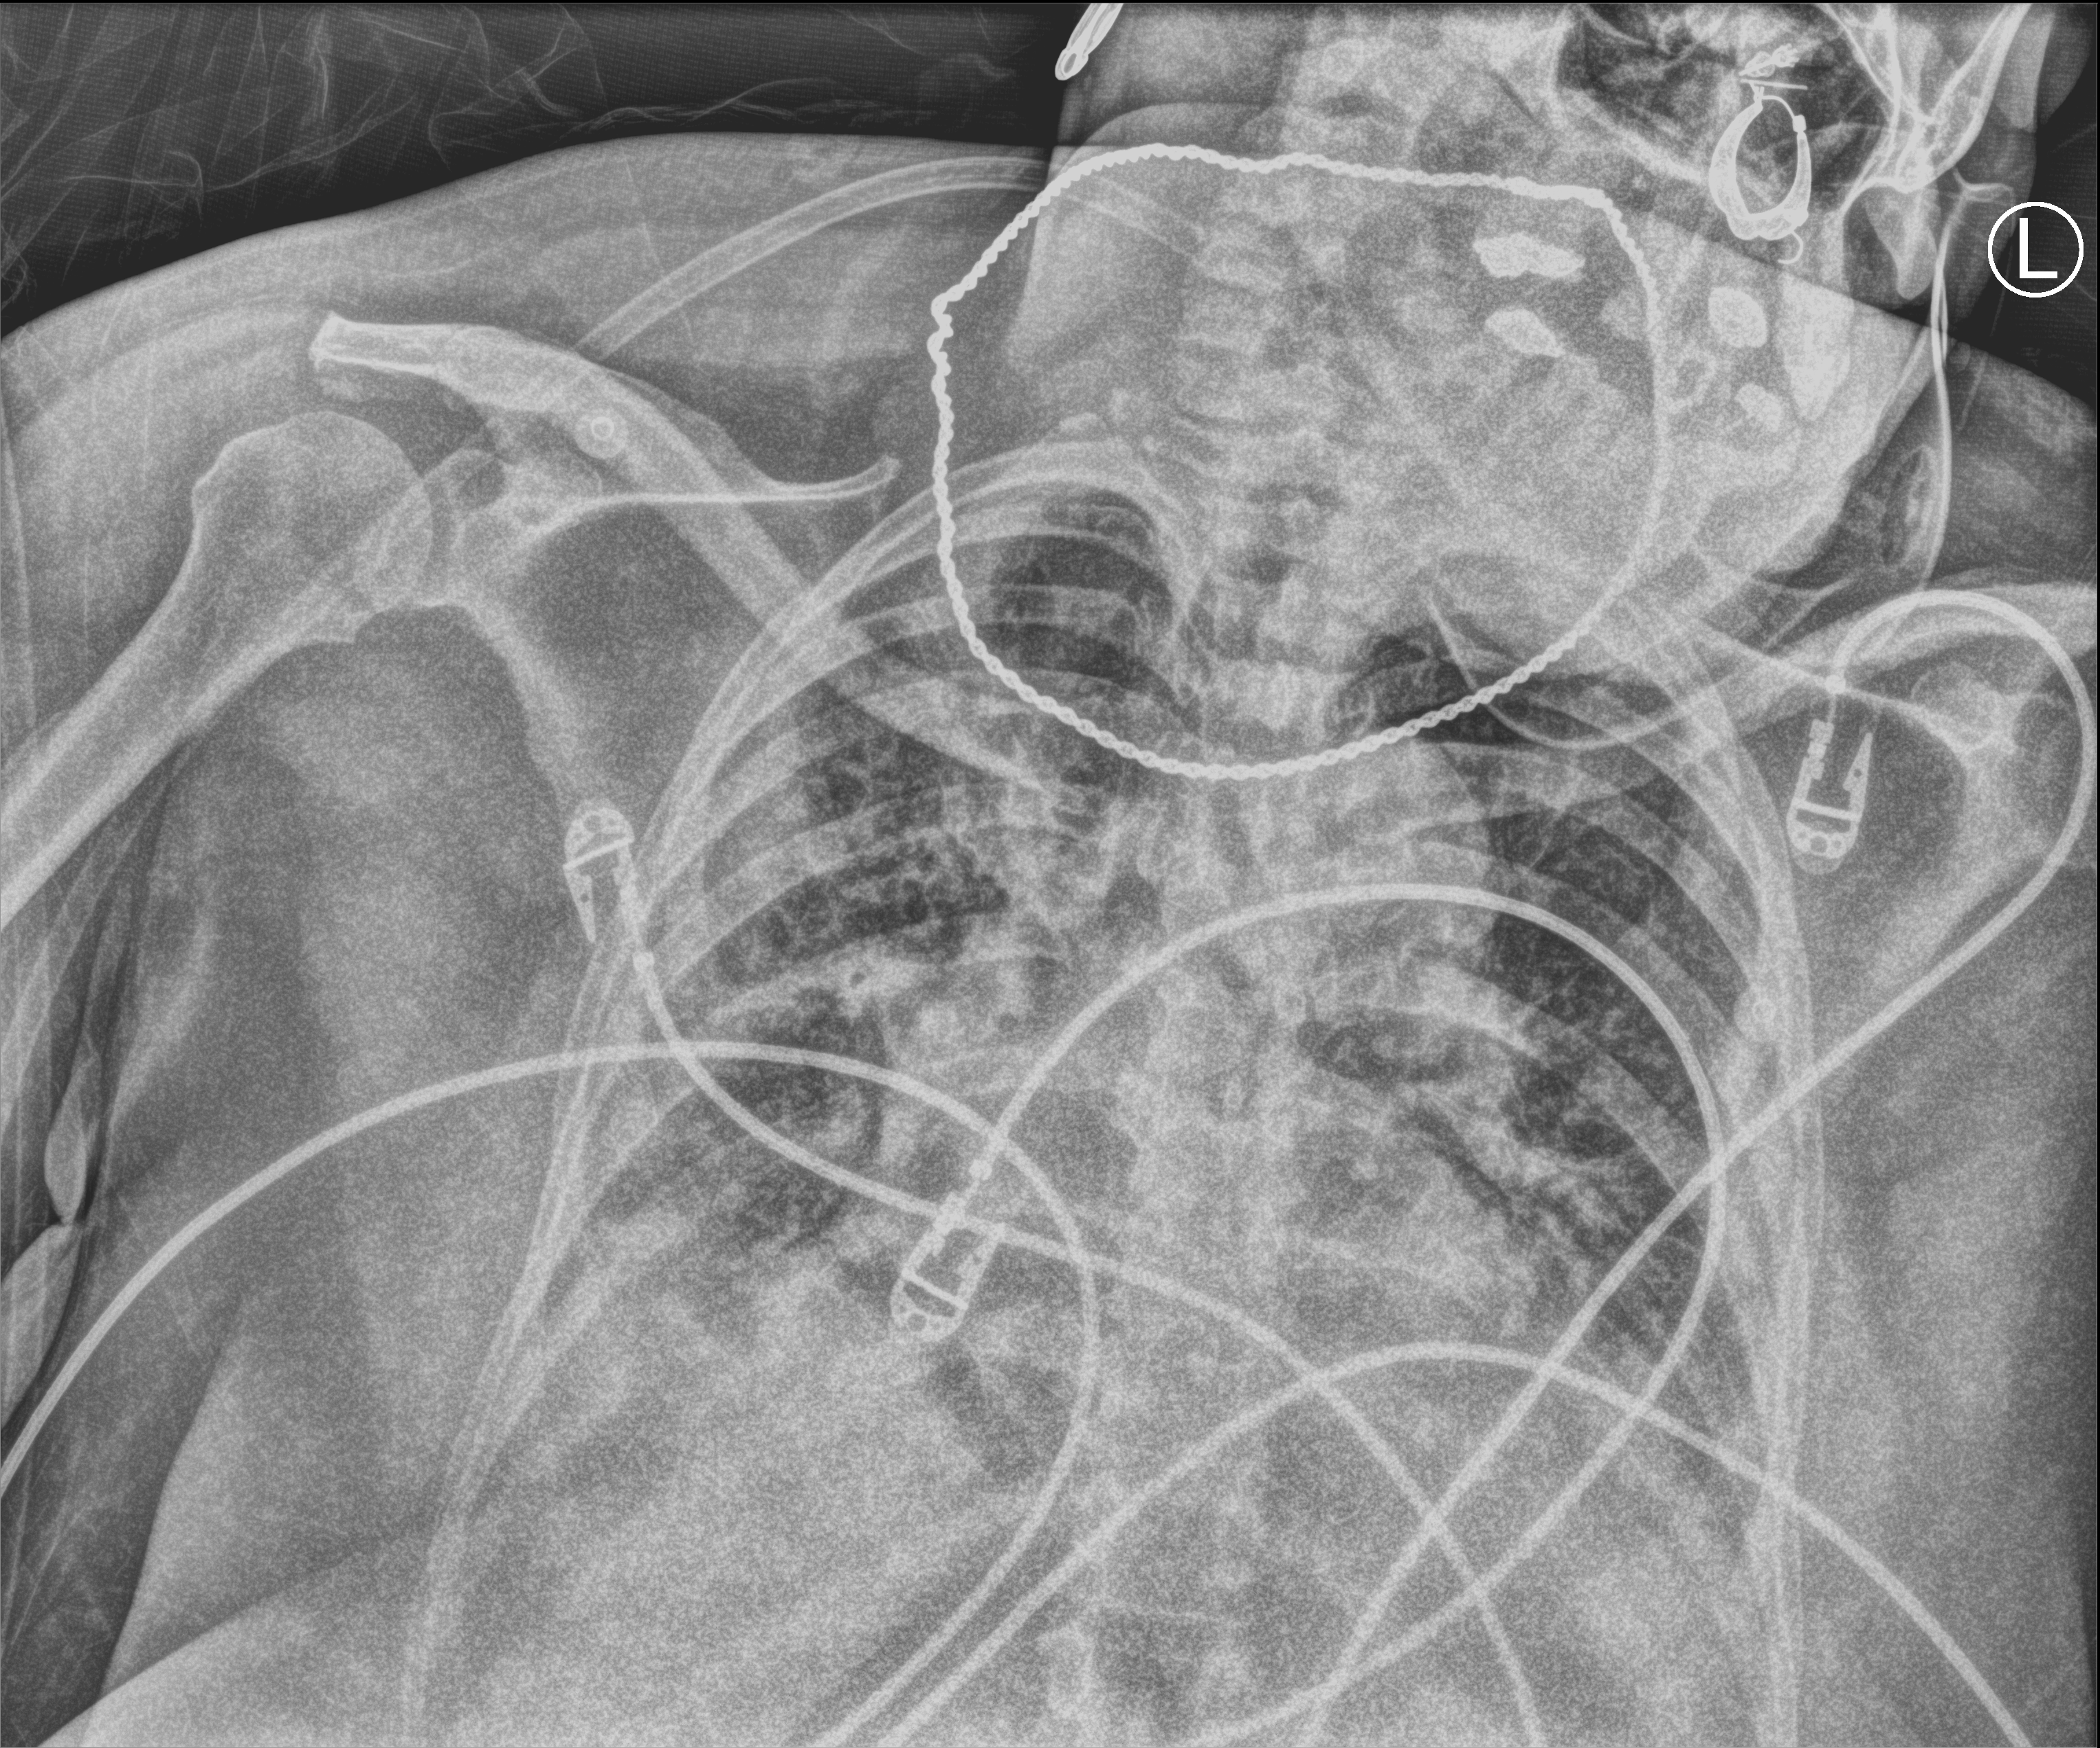
Bedside chest radiograph (computed radiography). Female patient hospitalised with COVID-19, age 60–74 years.
Hospital-stay facts (about this admission, not read from this image; timing relative to this image not recorded): admitted to intensive care during this hospital stay: yes; mechanically ventilated during this hospital stay: yes; chronic kidney disease (admission record): no.